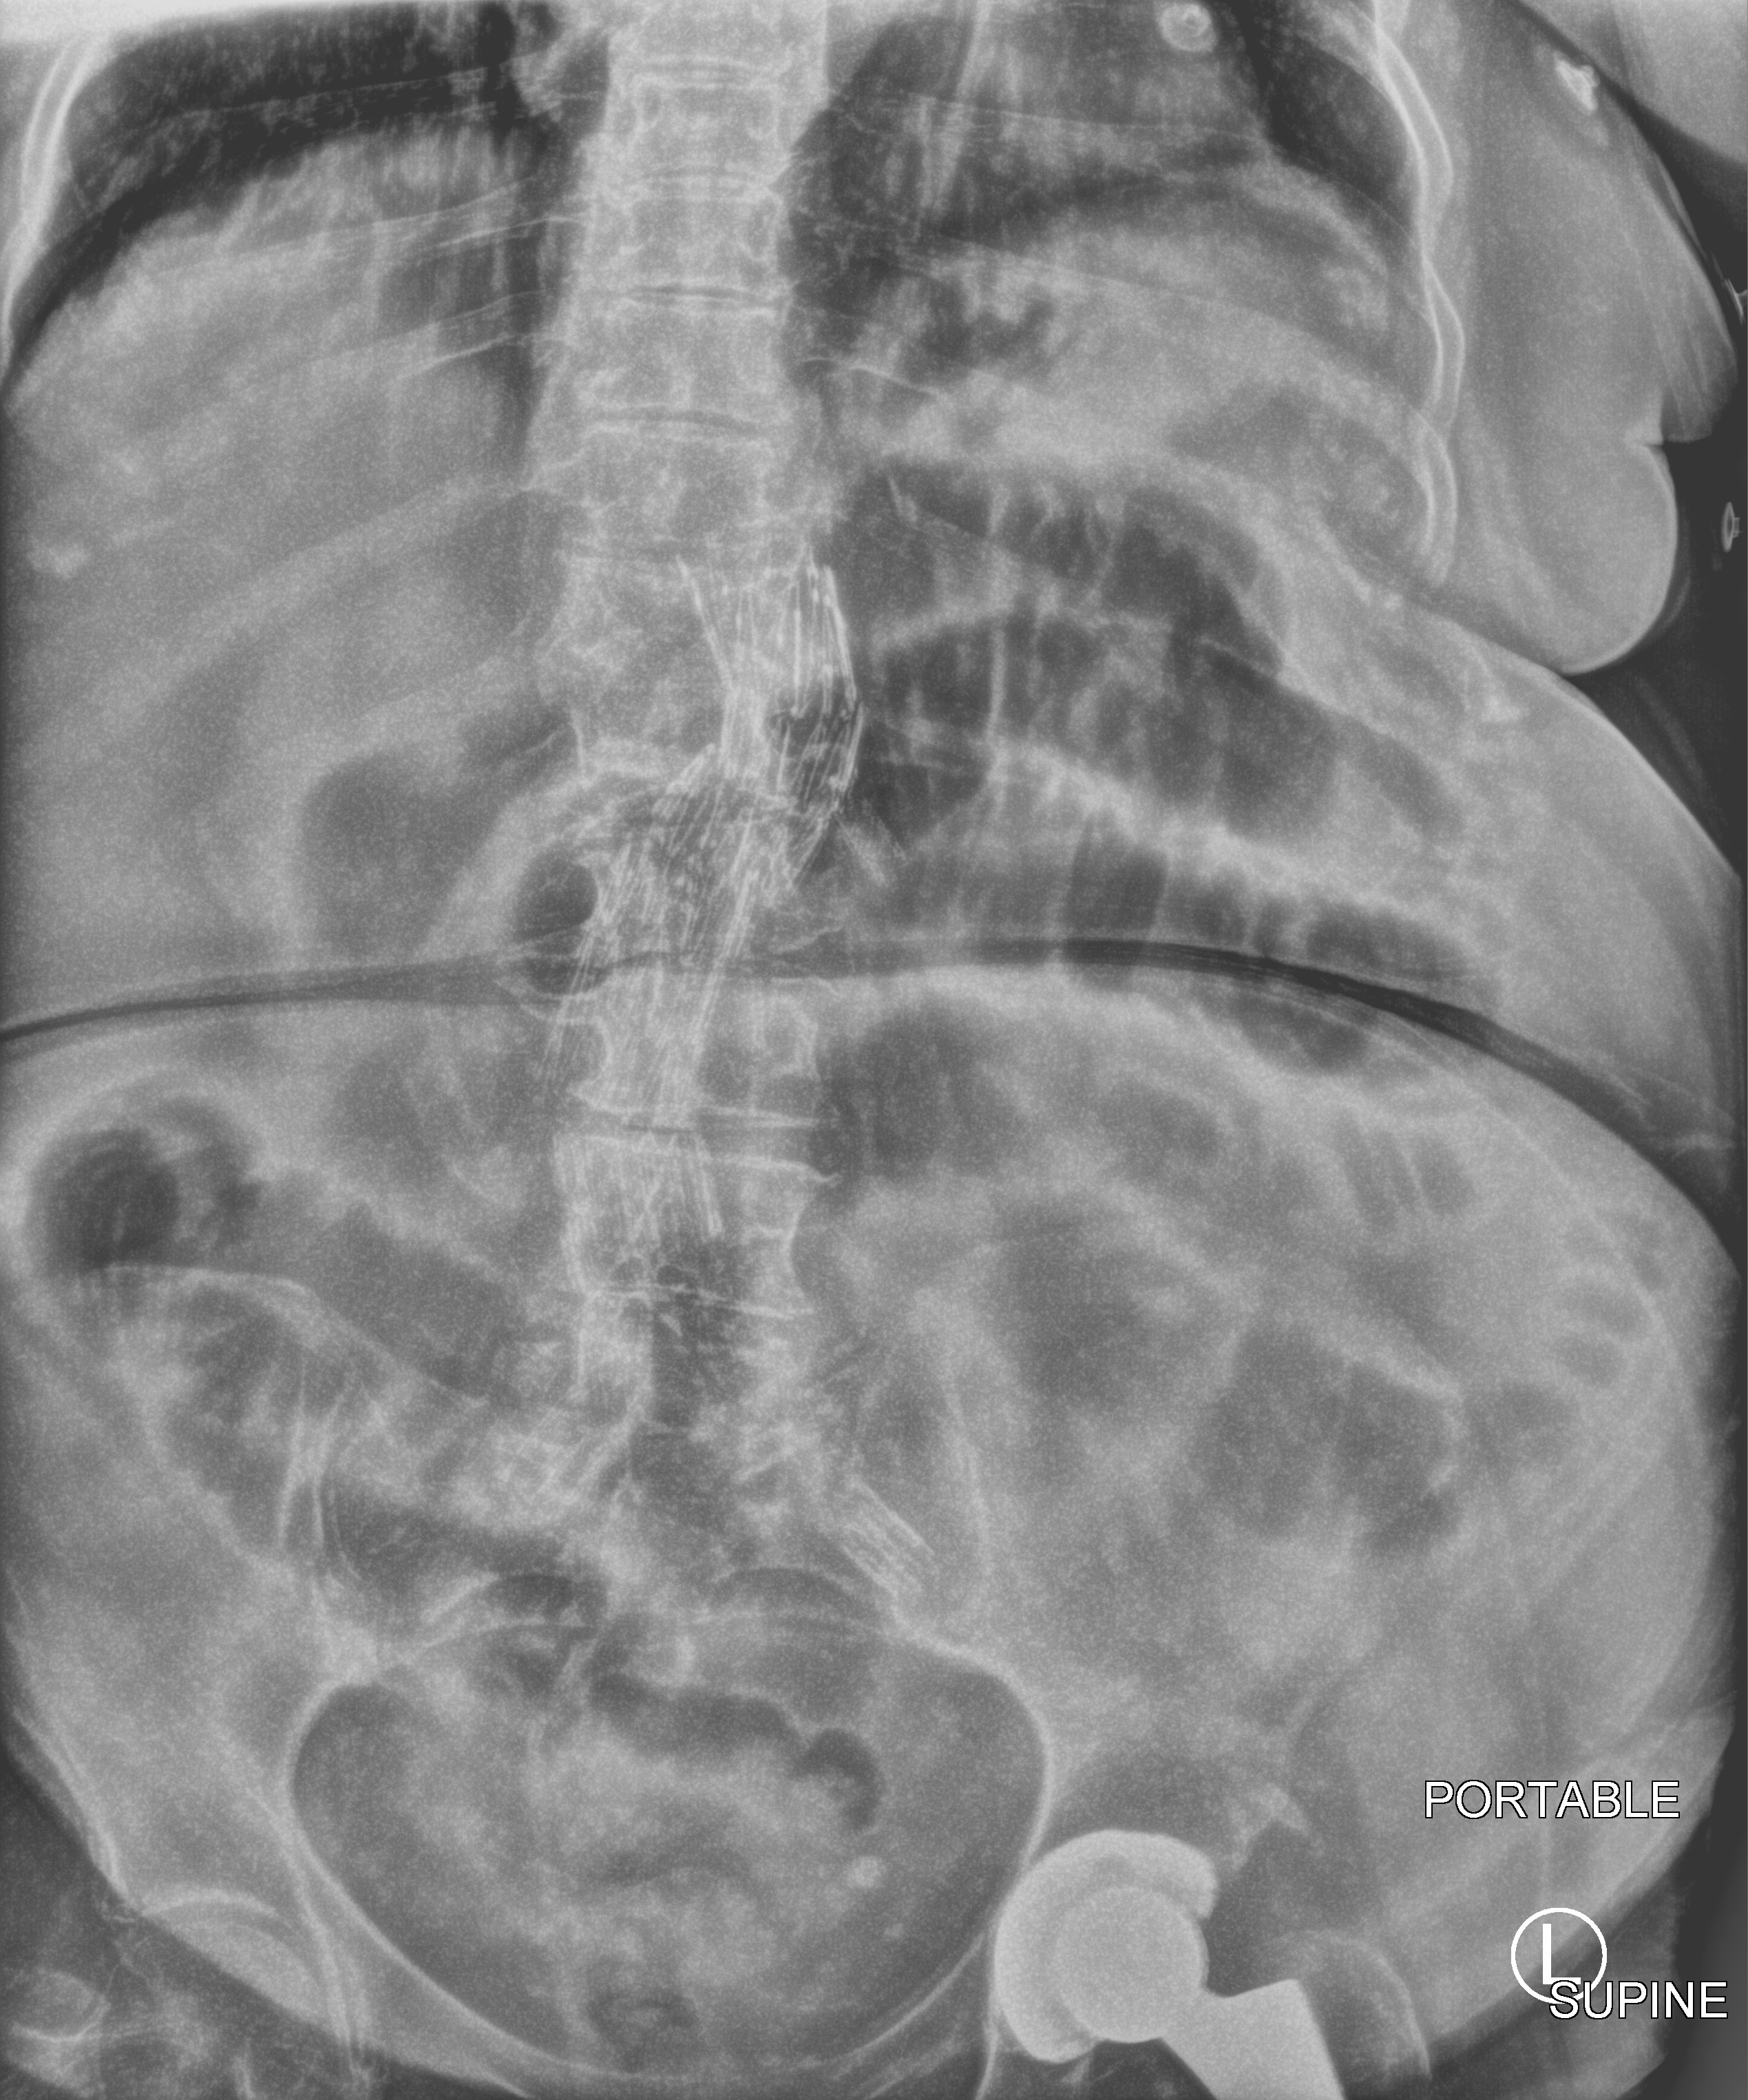
Bedside abdomen radiograph (computed radiography). Patient hospitalised with COVID-19; female, aged 60–74 years.
Hospital-stay facts (about this admission, not read from this image; timing relative to this image not recorded): admitted to intensive care during this hospital stay: yes; mechanically ventilated during this hospital stay: no.